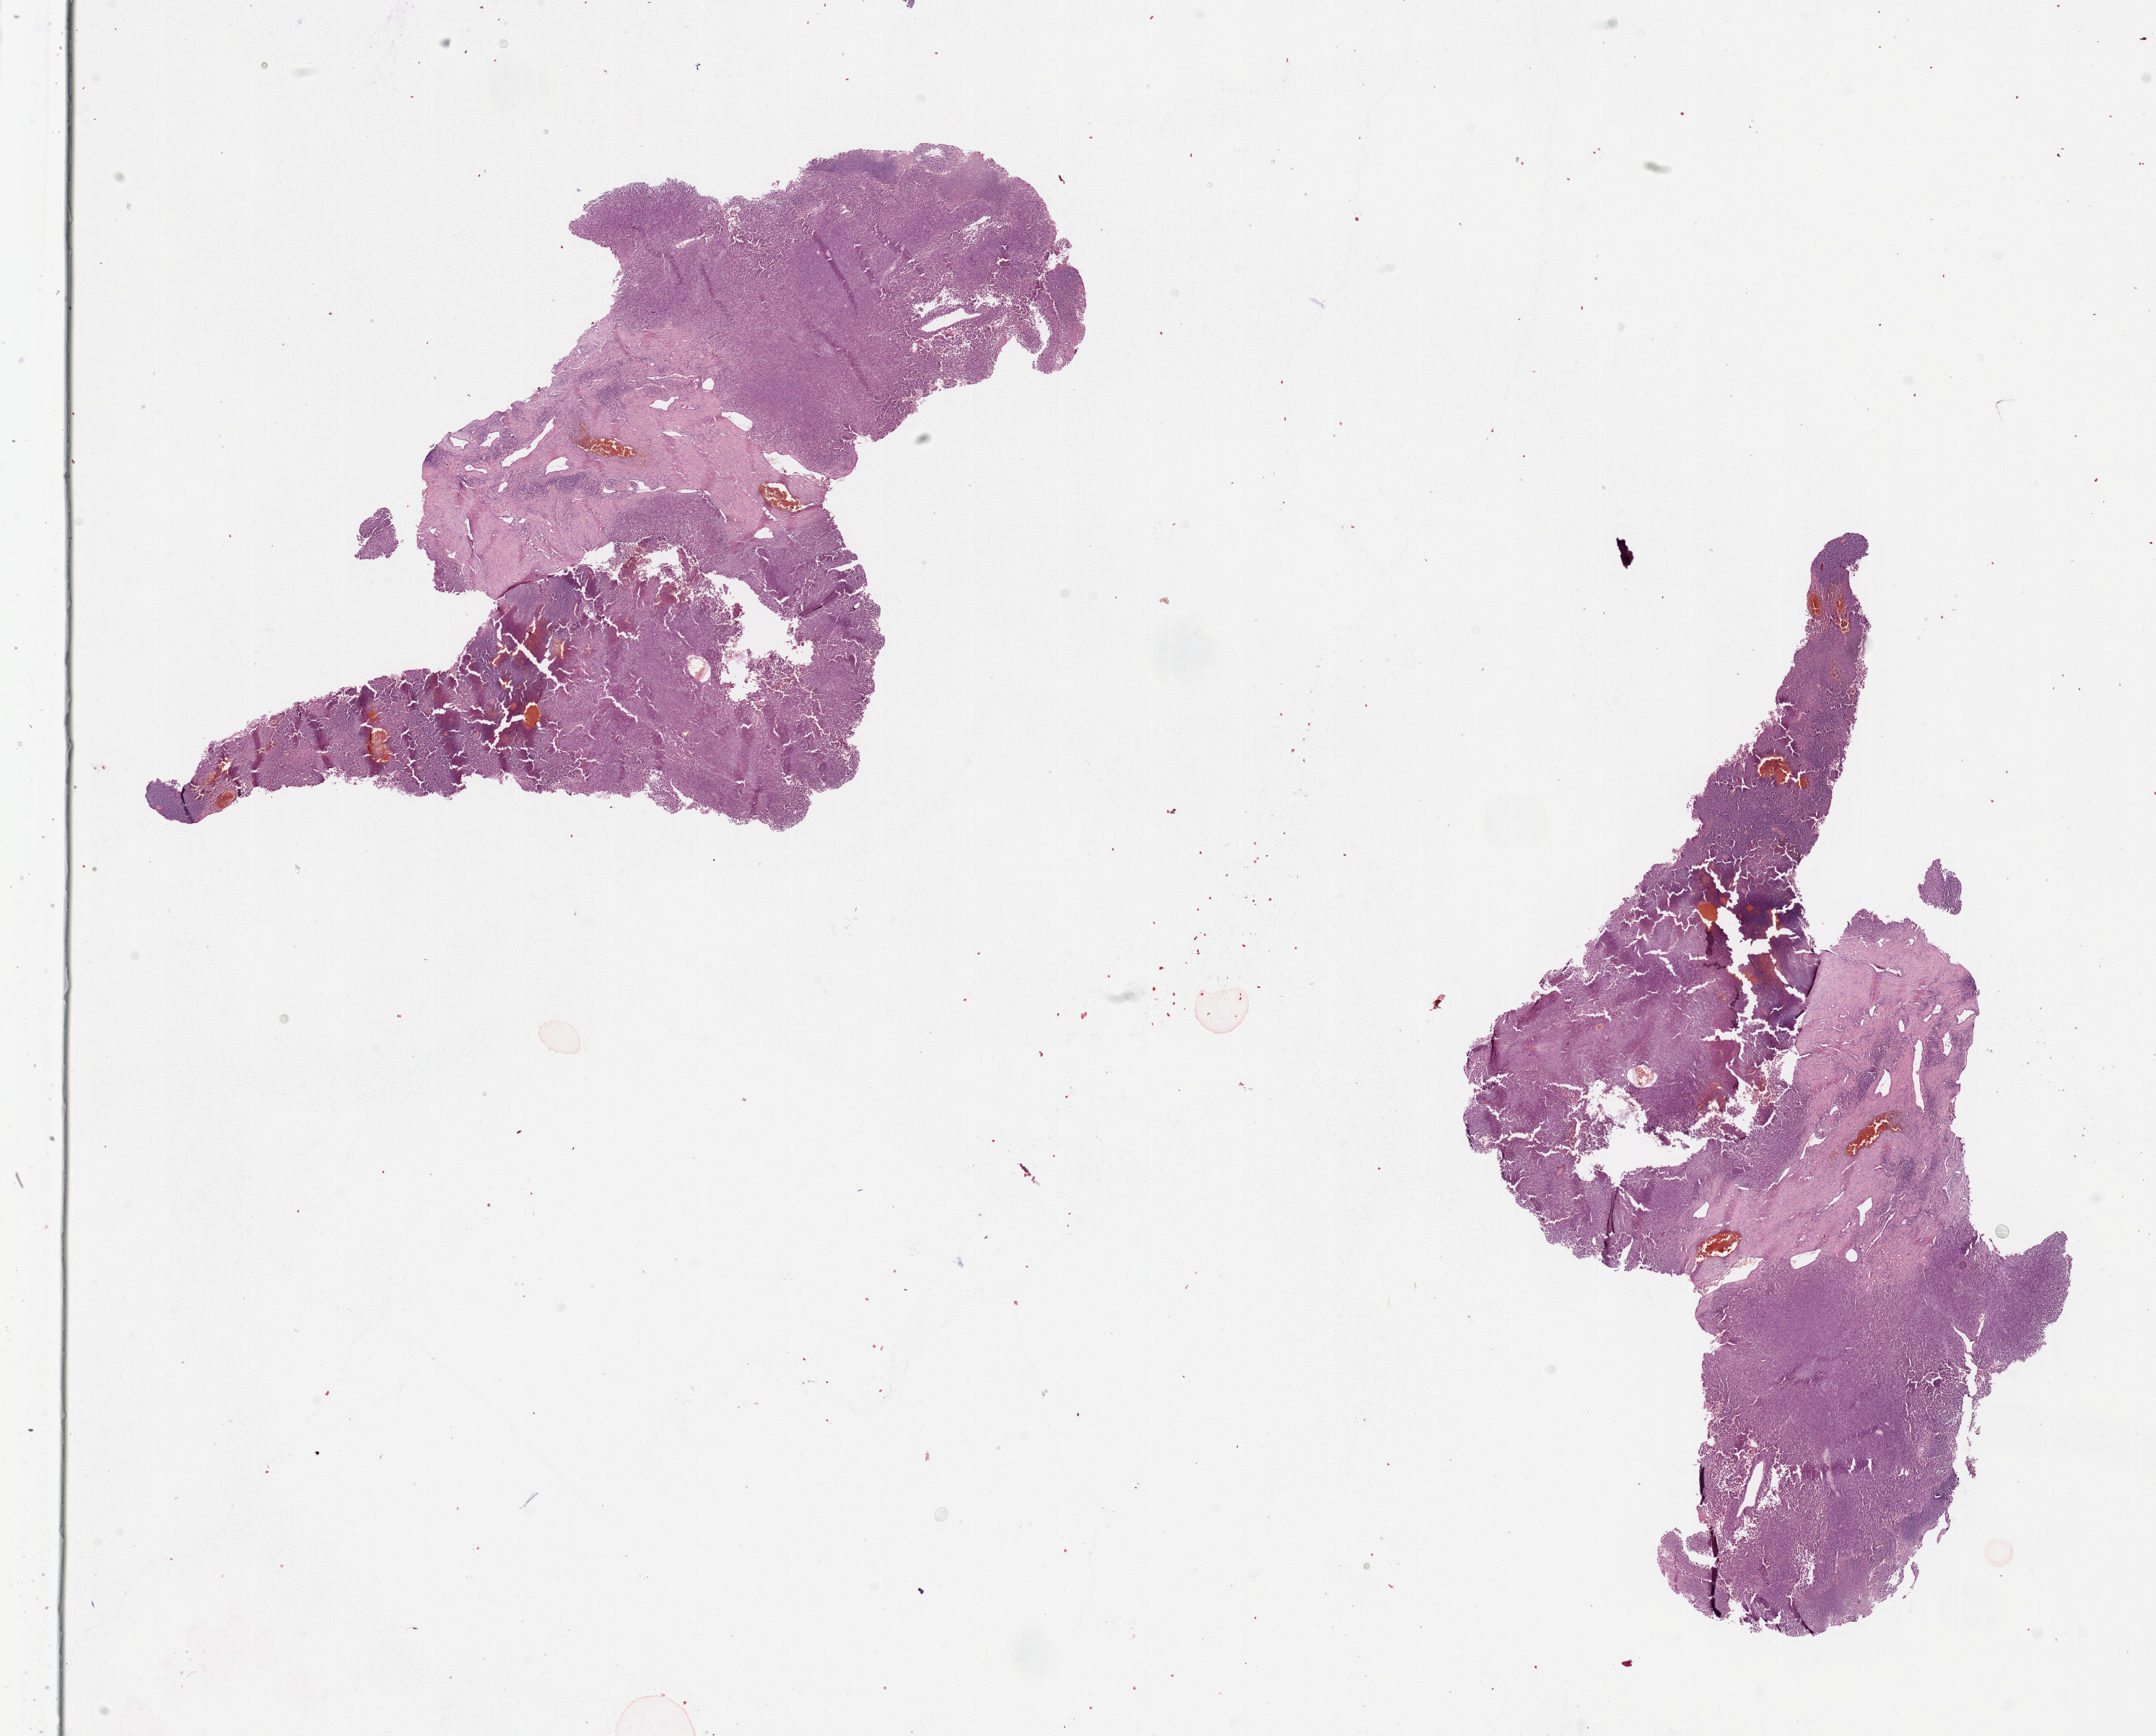
H&E whole-slide image — low-resolution overview of the scanned area, about 23.6 x 19.0 mm. Tumour tissue sample, sampled site: trunk. Male, 75 y/o. Pathologist review of this section (percent, as recorded): tumour nuclei 90%, necrosis 0%.
• AJCC pathologic stage: IIC
• primary tumour site (as recorded): trunk
• histologic diagnosis: Malignant melanoma, NOS